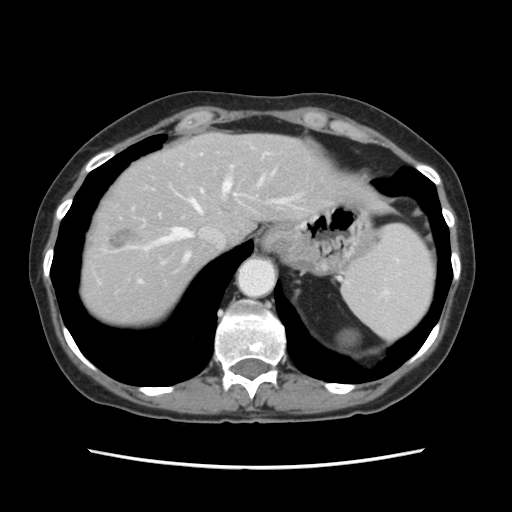
Contrast-enhanced abdominal CT, one axial slice; slice 98 of 120 in the series (ordered by position); 120 kVp; soft-tissue window (W 400 / L 40 HU); 512 × 512 image matrix, field of view 330 × 330 mm. Female patient, age 70 years. Case-level facts recorded for this patient, not image findings: diagnosis: colorectal cancer liver metastases, imaged before liver resection; multiple liver metastases: no; largest metastasis: 2.5 cm; chemotherapy before resection: yes.
Outlined on this slice (outlined manually by an expert reader):
- hepatic veins: bounding box (x1, y1, x2, y2) in pixels: (129, 167, 289, 263)
- liver: (83, 134, 356, 326)
- planned liver remnant (the part of the liver to remain after resection): (143, 133, 354, 267)
- portal vein (with intrahepatic branches): (139, 153, 268, 282)
- liver metastasis: (110, 229, 137, 249)